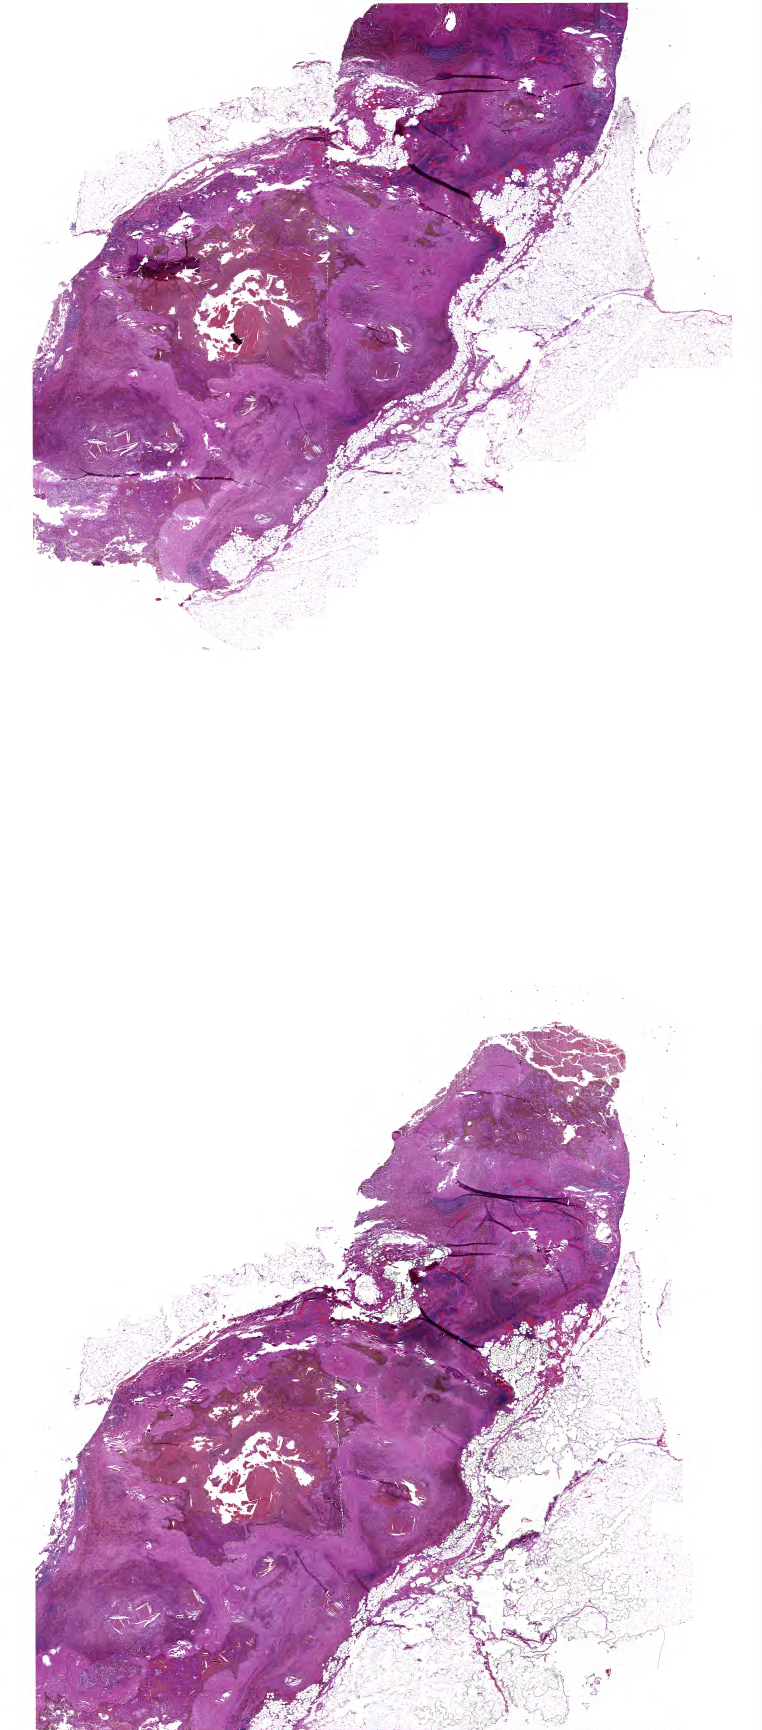
Whole-slide histology image, H&E-stained — shown as a low-resolution overview of the whole scanned area (about 19.0 x 43.1 mm, slide scanned at 40x), FFPE section, sample: primary tumour, kidney. Male, age 70 years at initial diagnosis.
• laterality: right
• pathologic diagnosis: Papillary adenocarcinoma, NOS